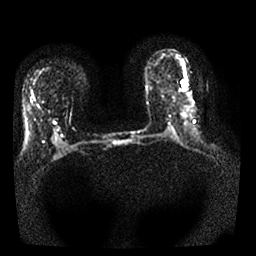
Breast MRI, one axial slice; position 14 of 25 along the scan axis; diffusion-weighted series; image 2 of 4 stored at this slice position (different b-values; order by instance number); 1.5 T; 256 × 256 image matrix, field of view 320 × 320 mm. Female patient.
Annotated regions visible in this slice (outlined manually by an expert reader):
- tumour on diffusion-weighted imaging: bounding box <182,81,186,89> (left, top, right, bottom; pixels)